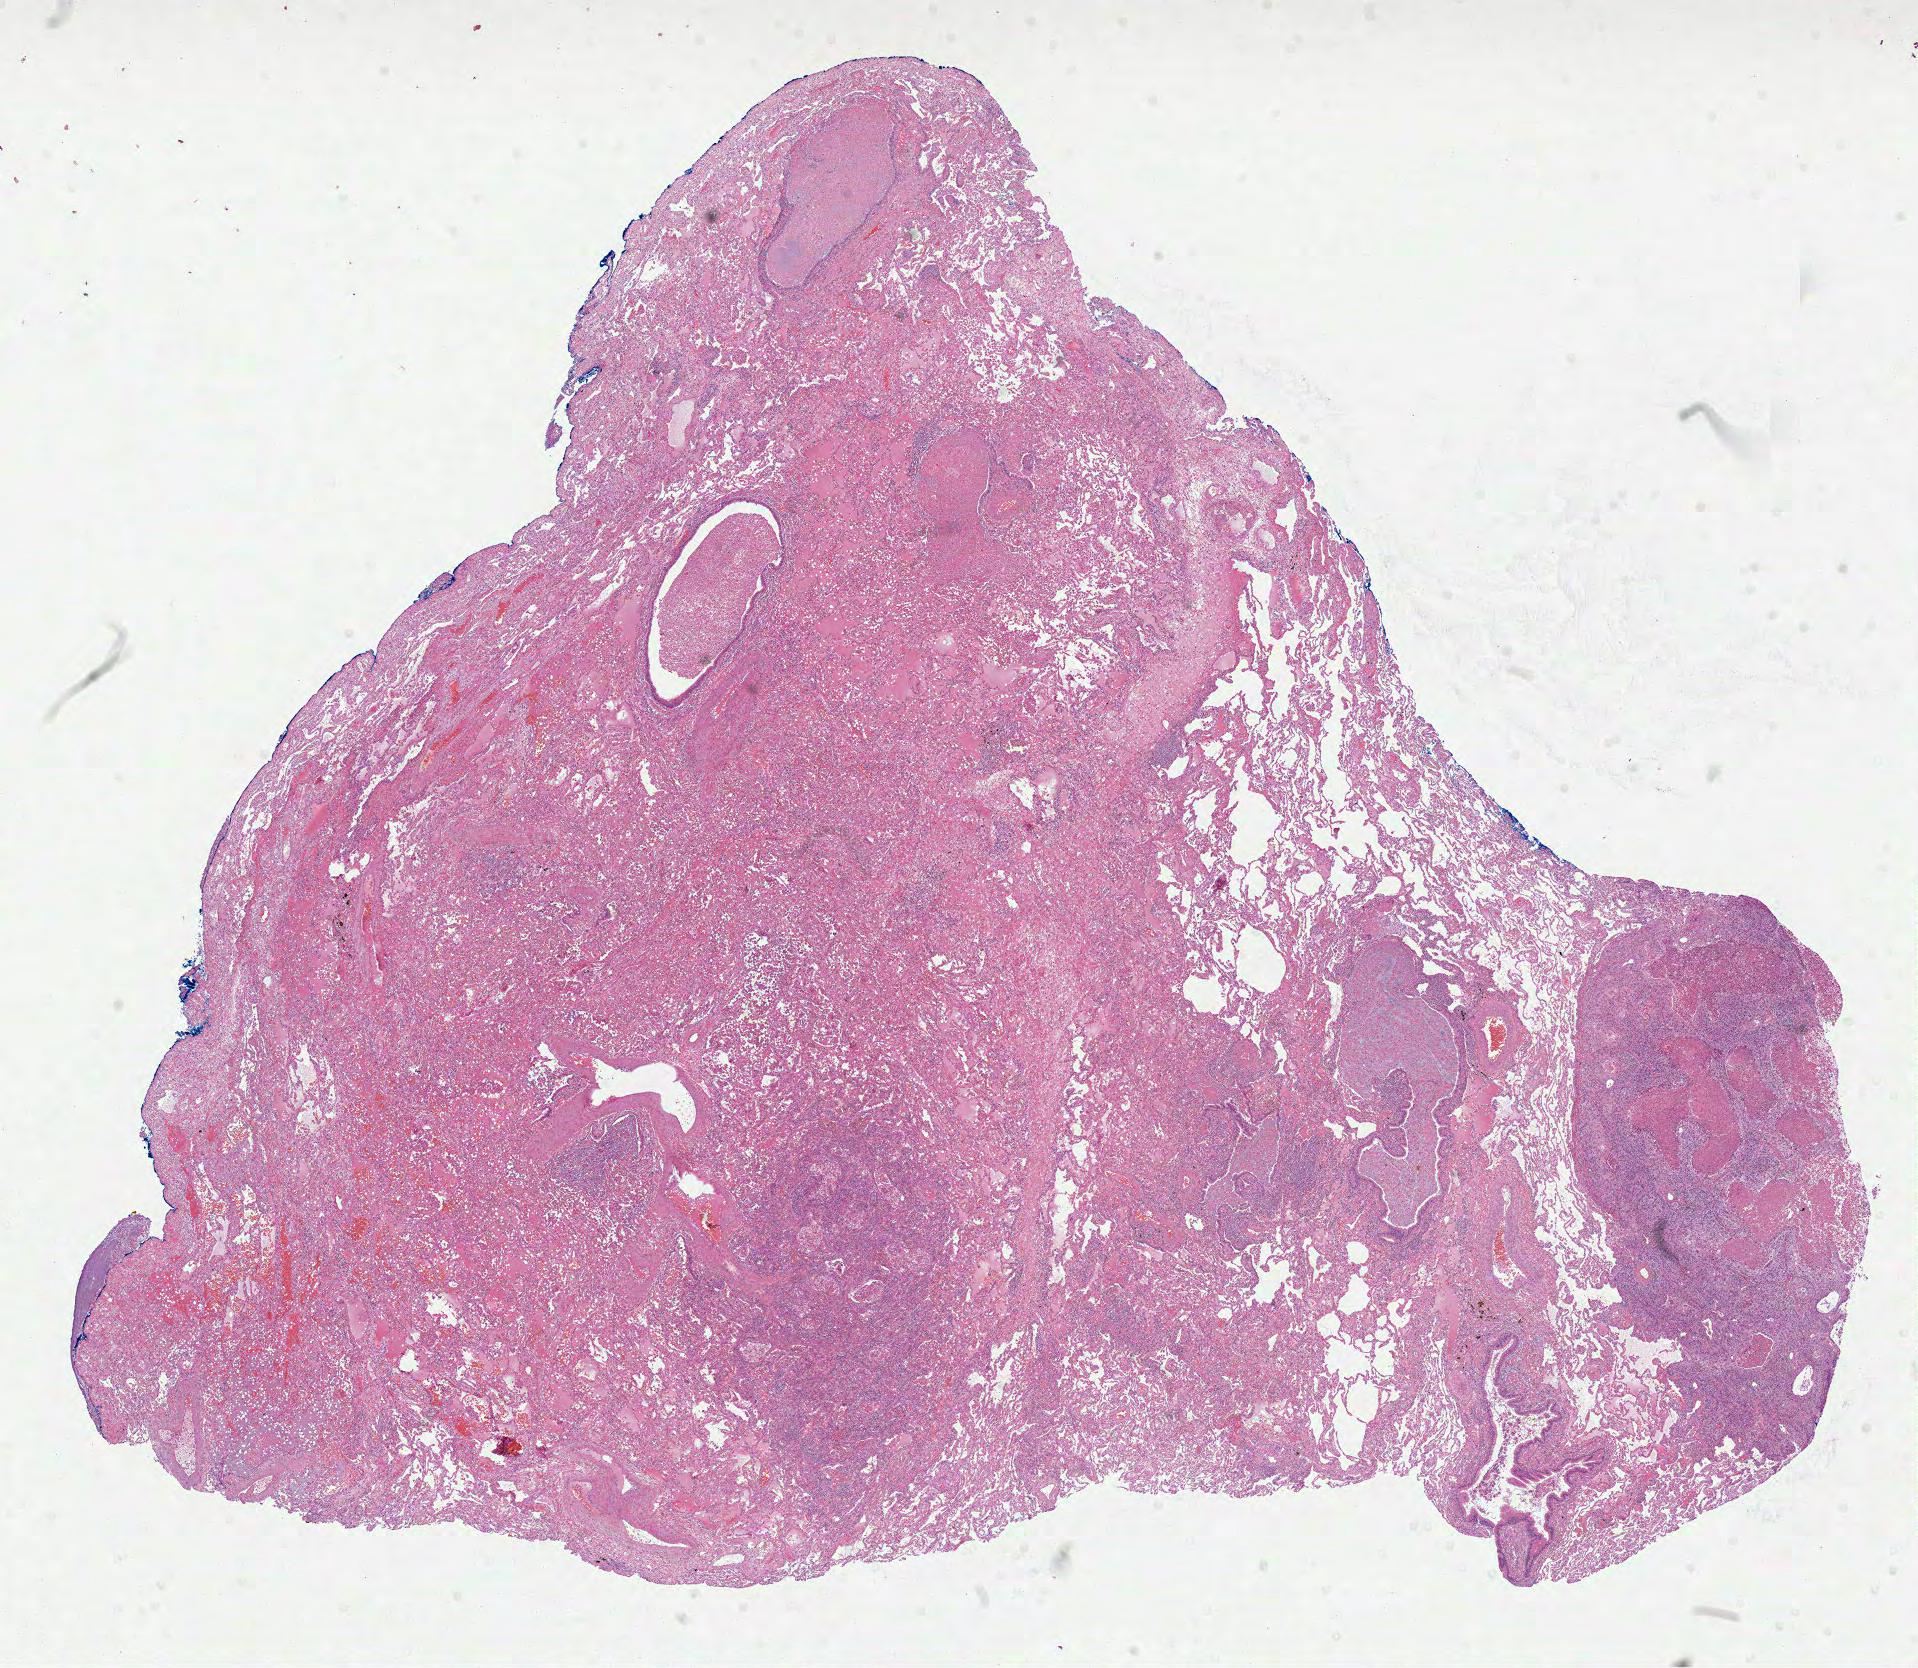
Digitized H&E tissue section (whole slide), shown as a low-resolution overview of the whole scanned area (about 15.5 x 13.5 mm, from a 40x scan); FFPE section; primary tumour sample from the lung. Male, age 73 years at initial diagnosis.
Pathologic diagnosis: Squamous cell carcinoma, NOS (upper lobe, lung). Laterality: right. AJCC pathologic stage: IIA (7th edition).